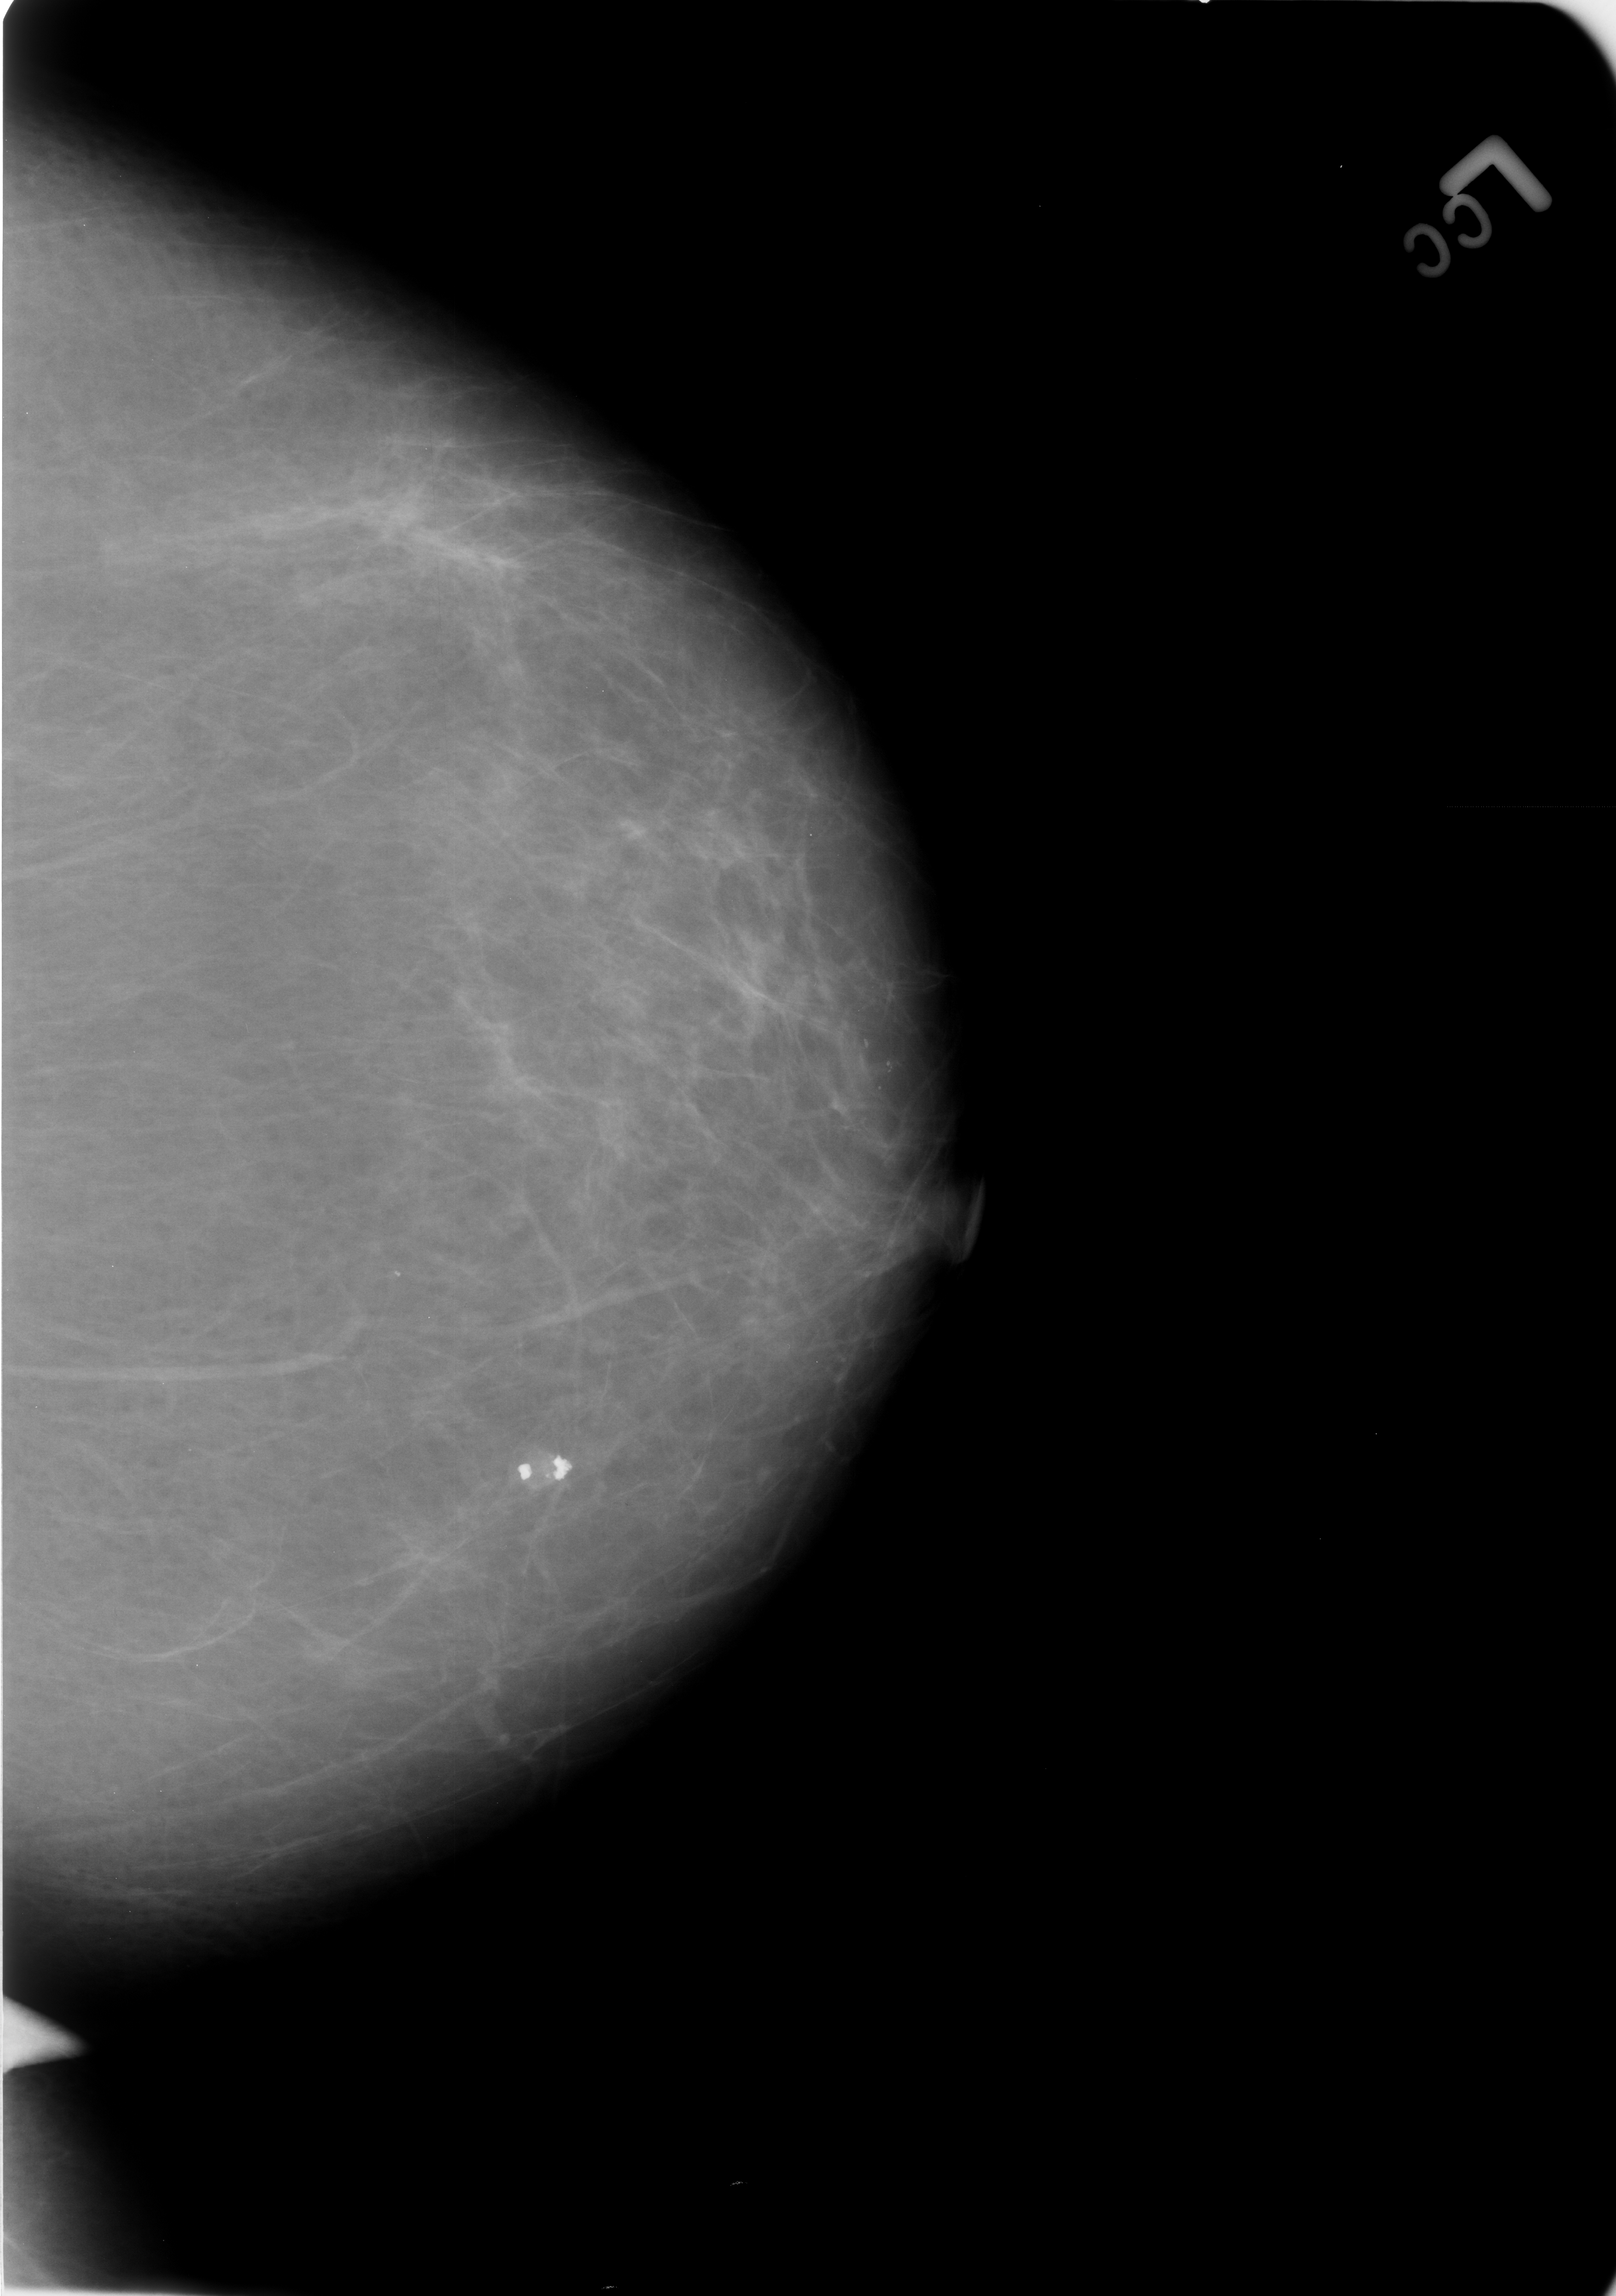
Scanned film-screen mammogram; left breast; craniocaudal (CC) view.
- Calcifications, morphology coarse; BI-RADS assessment category 2; benign without callback (not worked up further).